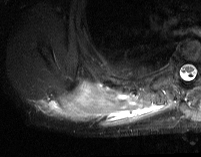
MRI of an extremity soft-tissue mass, one axial slice. Position 19 of 74 along the scan axis. STIR. MR volume resampled by the dataset authors to the PET/CT grid (not the native acquisition matrix). 3.27 mm slice thickness. 201 × 157 image matrix, field of view 196 × 153 mm. Male patient. Case-level facts recorded for this patient, not image findings: histological type: pleiomorphic spindle cell undifferentiated; grade: high; site of the primary tumour: right parascapusular.
Structures marked on this image (expert contour drawn on MRI and transferred to this co-registered scan by the dataset authors):
- gross tumour volume including surrounding oedema: box from (x=39, y=81) to (x=164, y=127) px
- gross tumour volume (mass): (x=65, y=82)–(x=107, y=119)